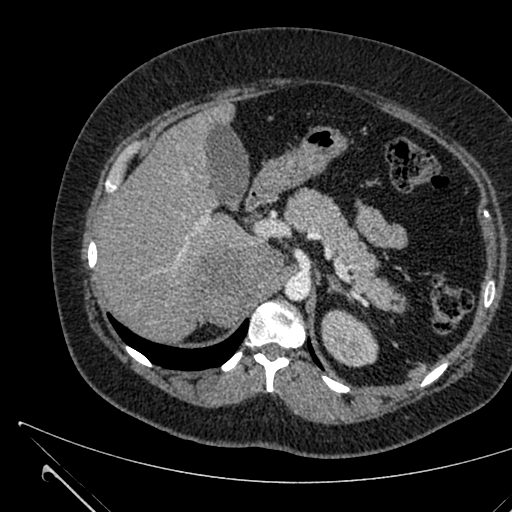
Contrast-enhanced abdominal CT, one axial slice; slice 446 of 731 in the series (ordered by position); intravenous contrast given; soft-tissue window (W 400 / L 40 HU); 512 × 512 image matrix. Patient: female, 36 years. From the clinical record (not read from this slice): diagnosis: adrenocortical carcinoma; tumour side: right adrenal.
Annotated regions visible in this slice (semi-automatically segmented with operator editing):
- mass: bounding box <196,245,282,324> (left, top, right, bottom; pixels)